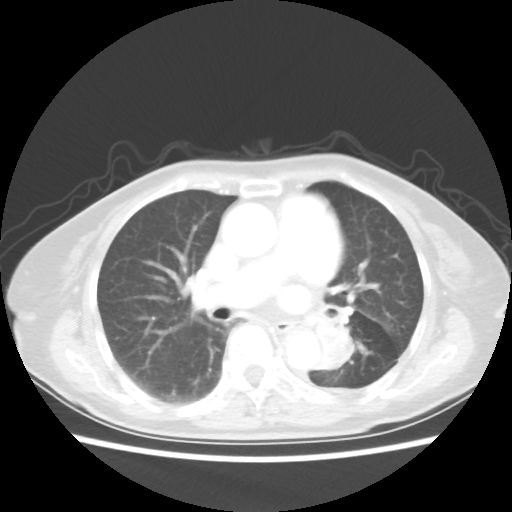
Chest CT, one axial slice; position 27 of 50 along the scan axis; reconstruction kernel STANDARD; lung window (W 1500 / L -600 HU); 512 × 512 image matrix, field of view 335 × 335 mm. Patient: female, 81 years. Case-level facts recorded for this patient, not image findings: clinical TNM (as recorded): T2 N0 M1a.
Structures marked on this image (rectangle marked by the reading radiologist):
- lung tumour (recorded histology: squamous cell carcinoma): bounding box [x1, y1, x2, y2] px = [307, 315, 355, 376]